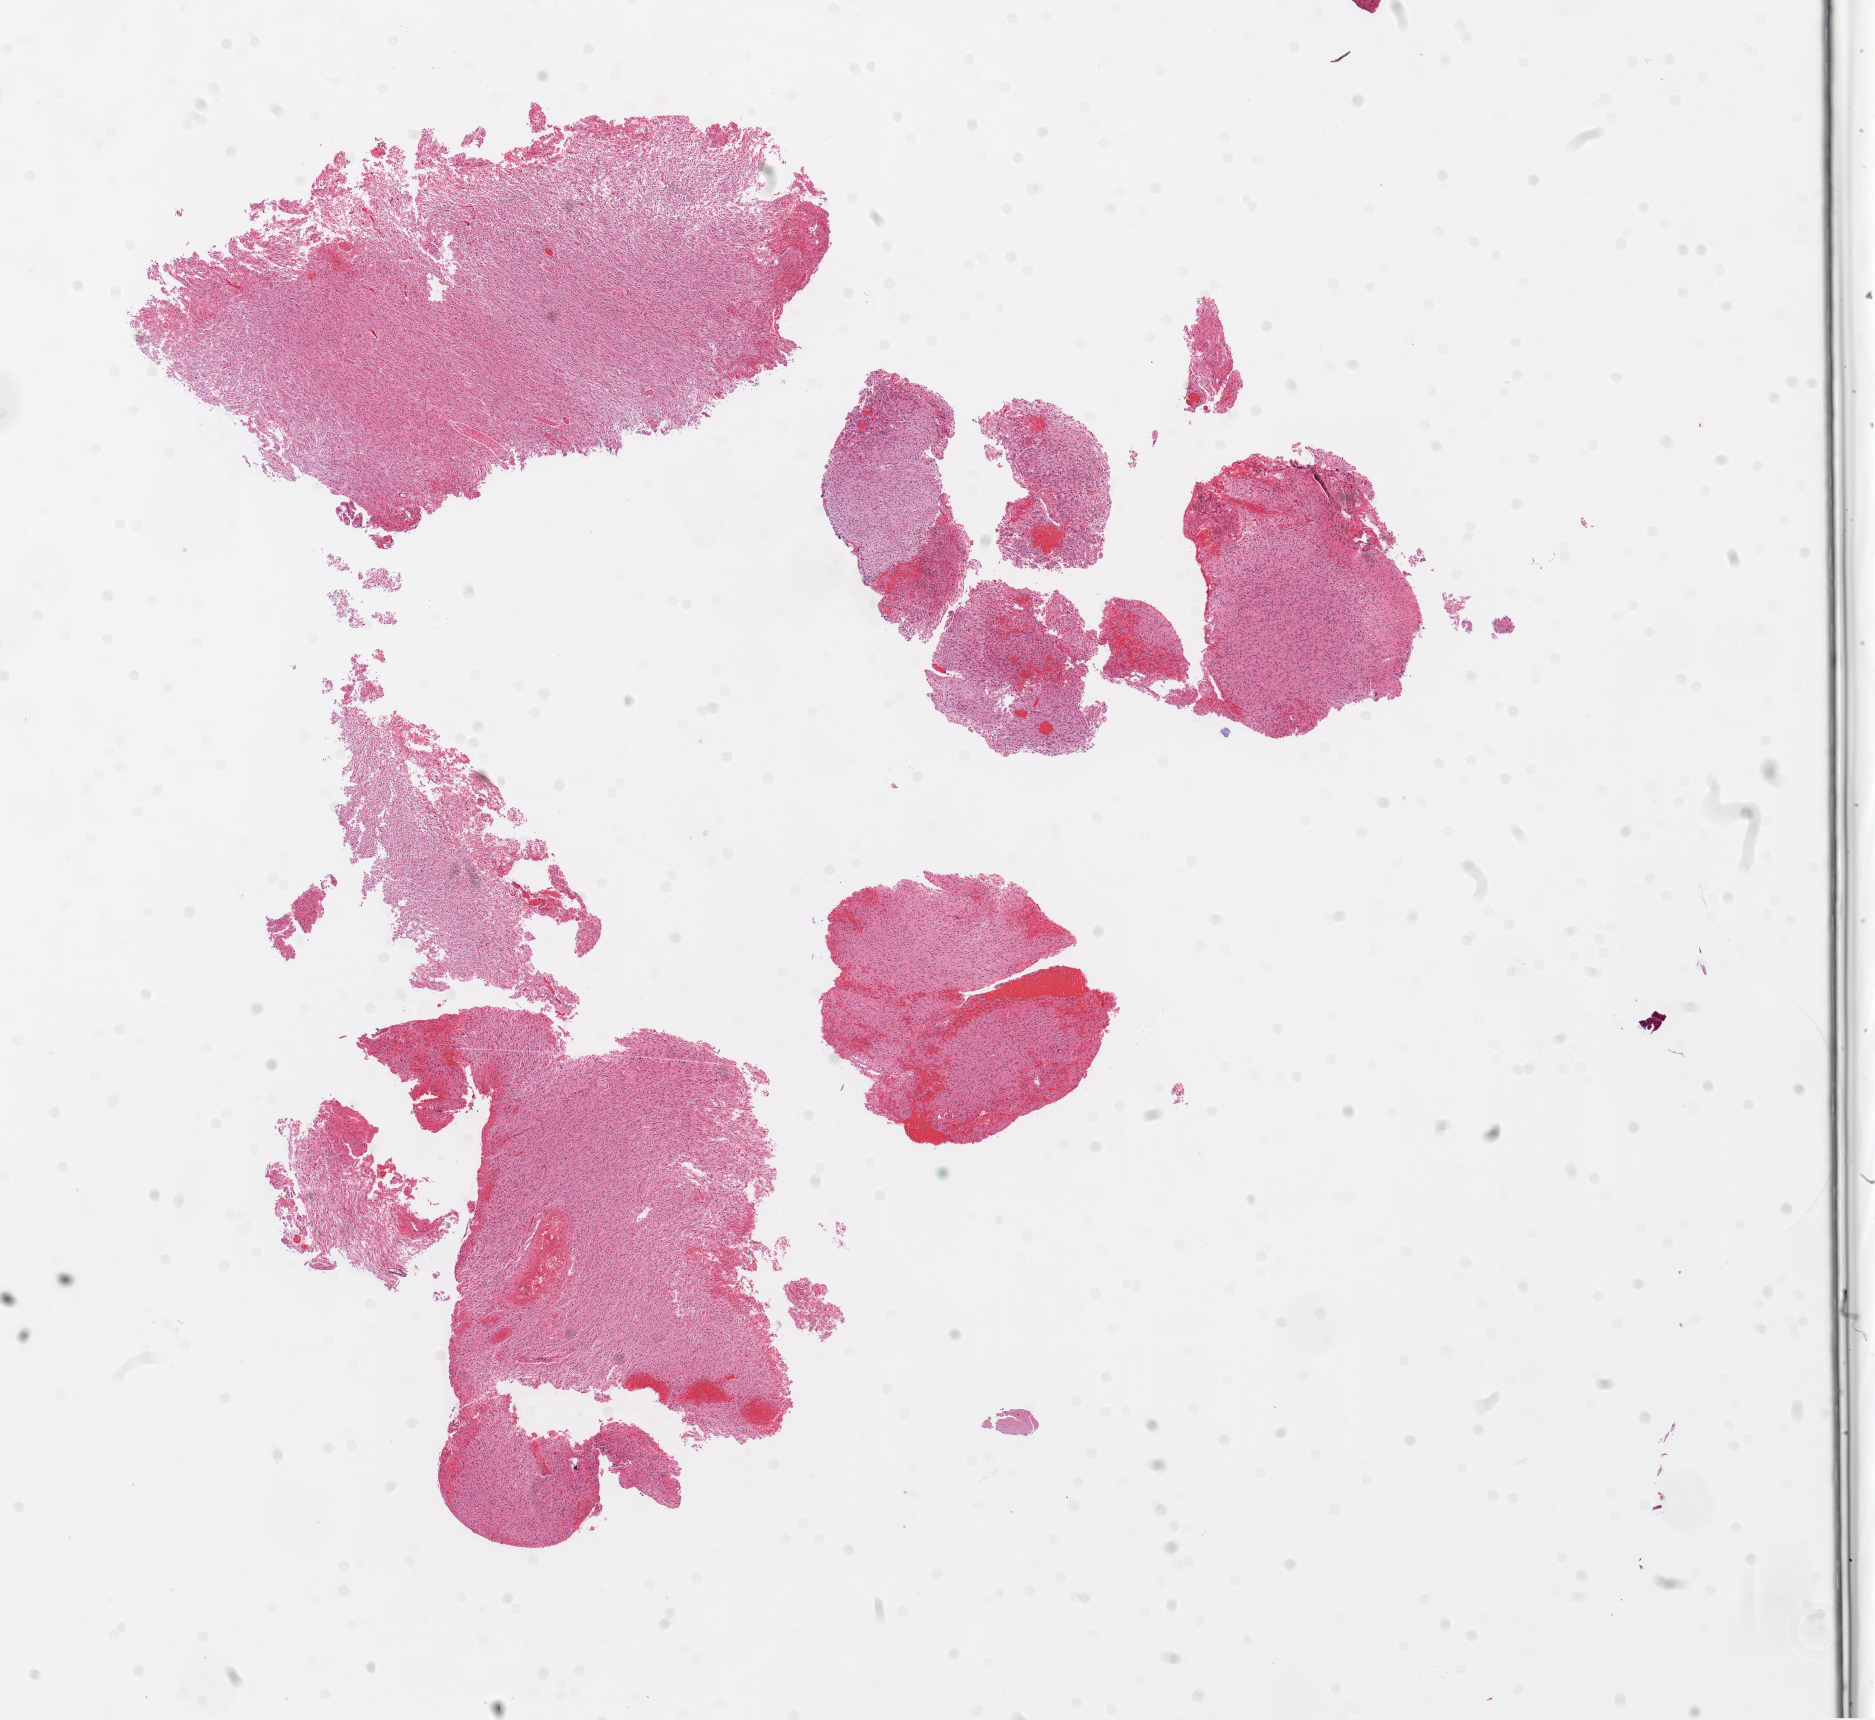
Digitized H&E-stained tissue section (whole slide), whole scanned area (about 15.0 x 13.8 mm, slide scanned at 20x) shown as a low-resolution overview; formalin-fixed paraffin-embedded (FFPE) diagnostic section; brain, primary tumour sample. Patient: male, age at initial diagnosis 50 years.
Diagnosis: Glioblastoma.